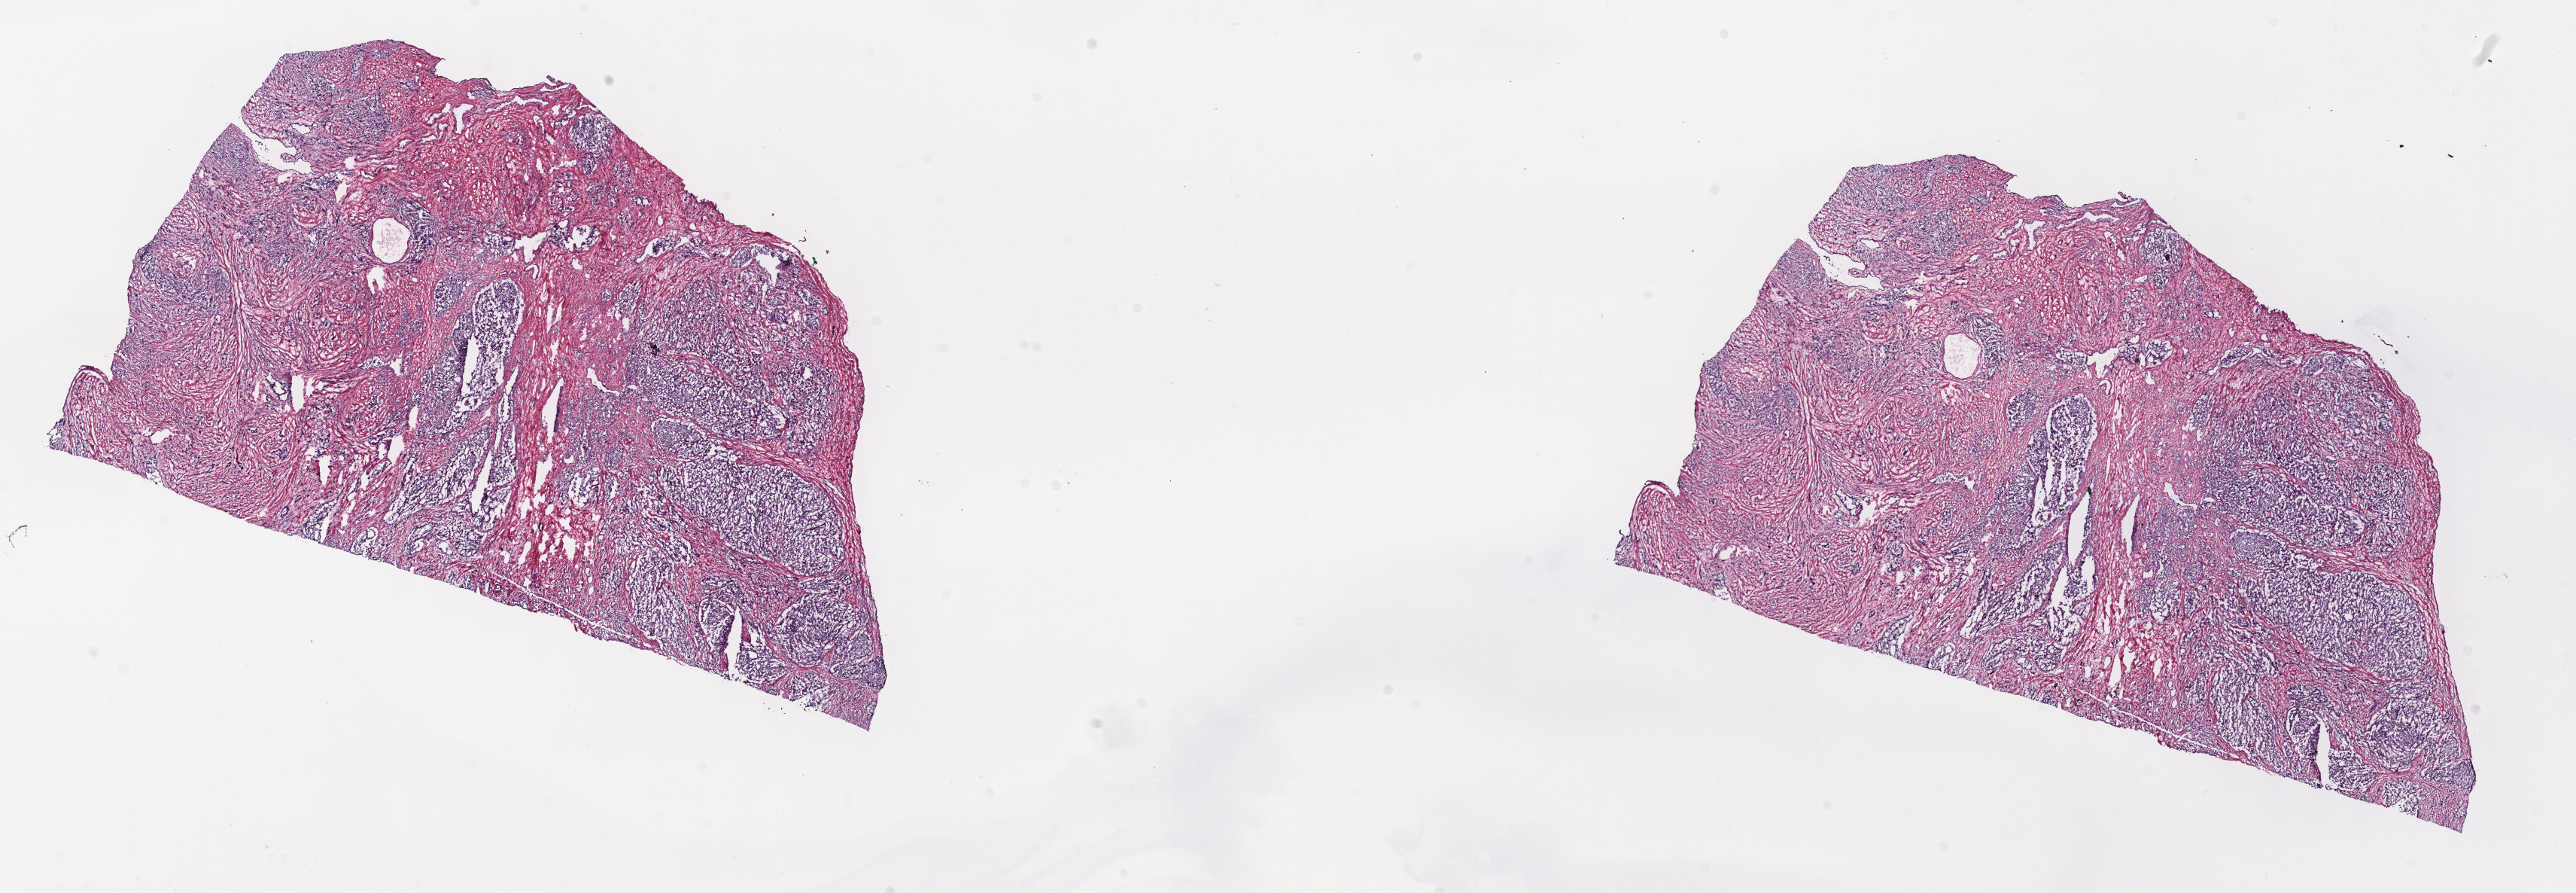
Digitized Hematoxylin and eosin (H&E) stained tissue section (whole slide) — low-resolution overview of the scanned area, about 27.7 x 9.6 mm, frozen section, sample: primary tumour, prostate. Male patient; age at initial diagnosis 70 years. Gleason score: 9 (5+4). Pathologist review of this section (percent, as recorded): tumour cells 50%, tumour nuclei 60%, normal cells 50%, stromal cells 0%, necrosis 0%. Inflammatory infiltration, as recorded: lymphocyte infiltration 0%, monocyte infiltration 0%, neutrophil infiltration 0%.
* laterality: bilateral
* histologic diagnosis: Adenocarcinoma, NOS (prostate gland)
* lymph nodes positive (case pathology): 2 of 19 examined